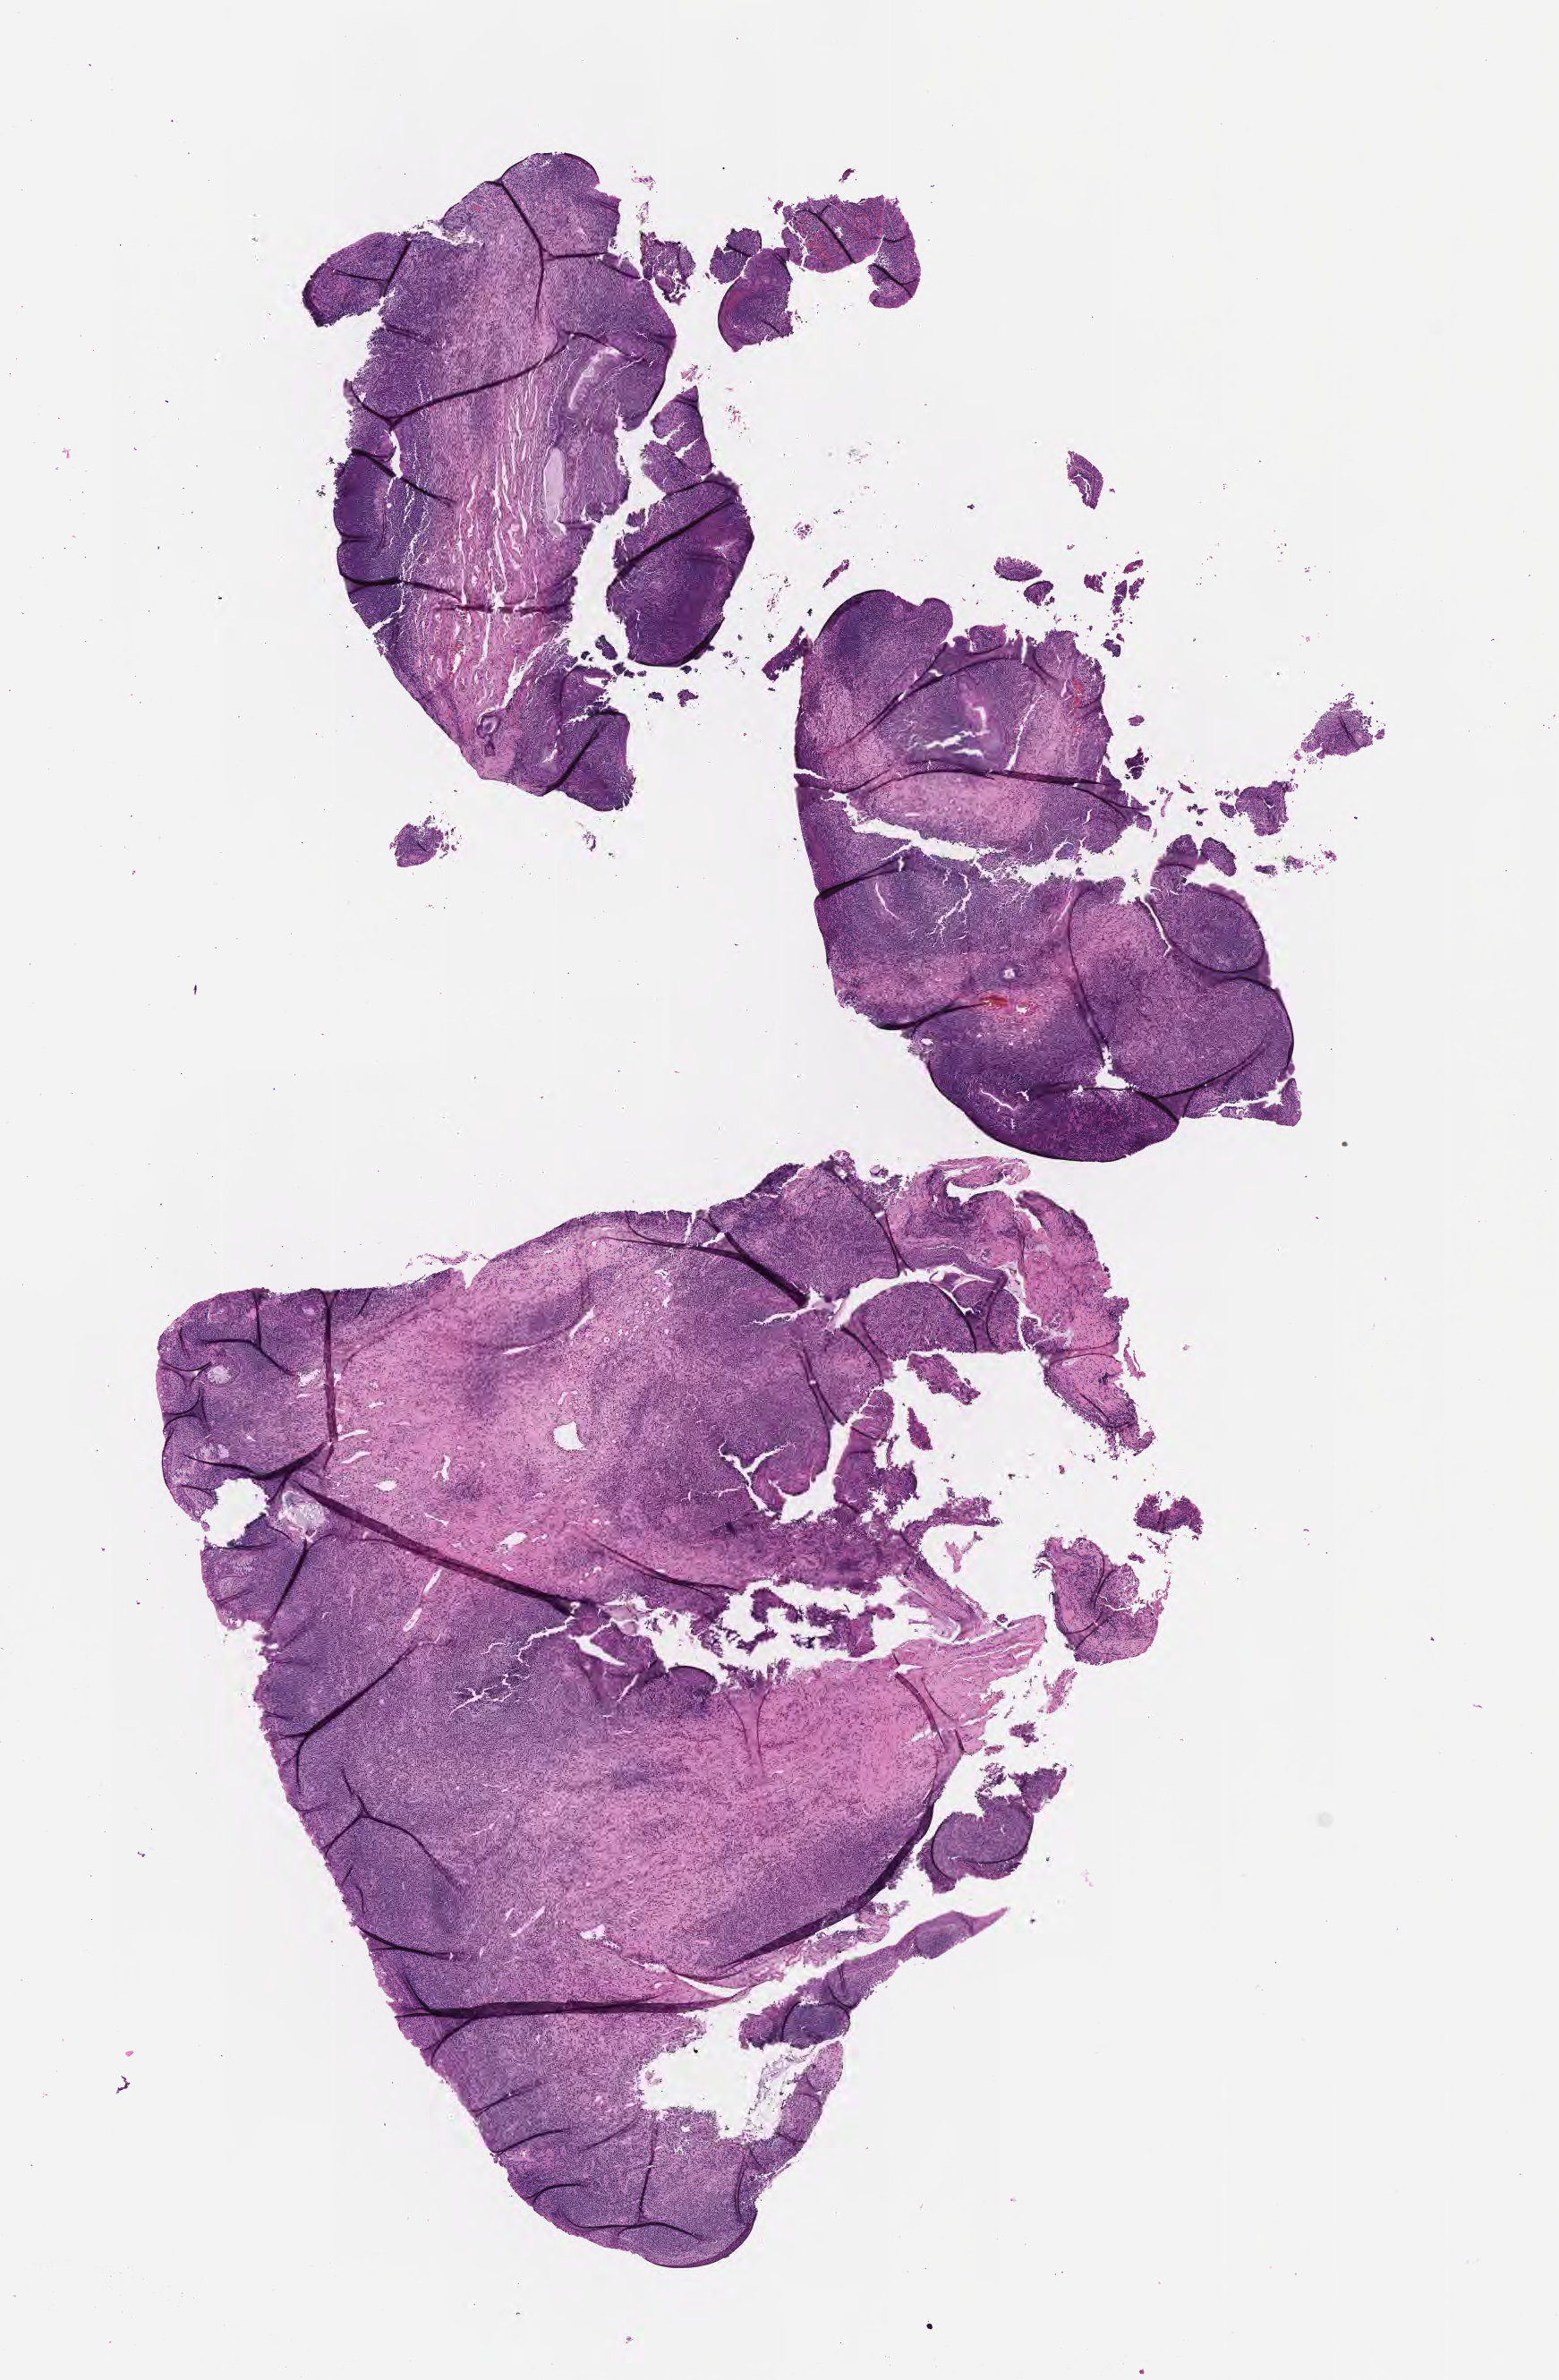
Whole-slide image, hematoxylin and eosin (H&E) stain, whole scanned area (about 7.0 x 10.8 mm) shown as a low-resolution overview. FFPE section. Normal-tissue sample (non-tumor) from a patient with burkitt lymphoma, NOS. Male patient; age at initial diagnosis 5 years. Composition of this section per pathologist review: tumor cells 0%, tumor nuclei 0%, stromal cells 0%, necrosis 0%, normal cells 100%. Inflammatory infiltration, as recorded: lymphocyte infiltration 80%, monocyte infiltration 10%, neutrophil infiltration 5%.
This section: non-tumor tissue sample; the patient's diagnosis is given above. Section: top of the tissue portion.